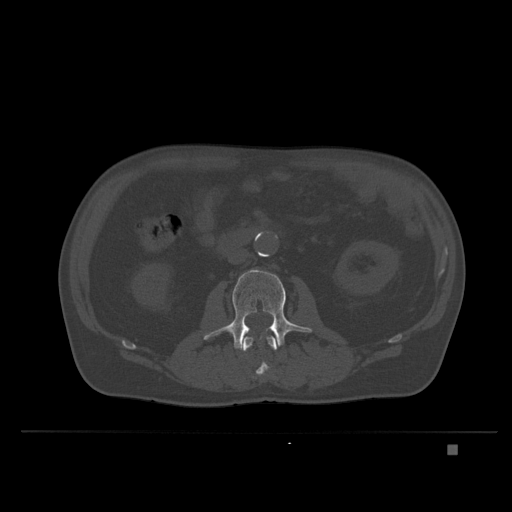
CT including the spine, one axial slice. Slice 102 of 435 in the series (ordered by position). Bone window (W 1800 / L 400 HU). 1.5 mm slice thickness. 512 × 512 image matrix, field of view 434 × 434 mm. Patient: male, 73 years. From the clinical record (not read from this slice): primary cancer: skin.
Outlined on this slice (semi-automatic segmentation, software-assisted and operator-edited):
- L2 vertebra: bounding box <243,333,278,378> (left, top, right, bottom; pixels)
- L3 vertebra: <204,269,312,350>